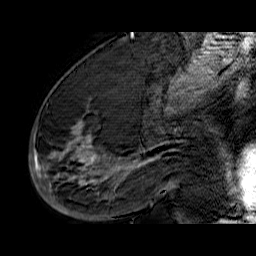
Breast MRI (dynamic contrast-enhanced), one sagittal slice; position 34 of 60 along the scan axis; dynamic contrast-enhanced series, time point 2 of 6 at this slice position (early post-contrast); 1.5 T; TE 6.5 ms, TR 32.9 ms; 4 mm slice thickness; 256 × 256 image matrix, field of view 200 × 200 mm. Female patient. Case-level facts recorded for this patient, not image findings: setting: breast cancer imaged before/during neoadjuvant chemotherapy; receptor status: HR-positive, HER2-negative.
Outlined on this slice (semi-automatically segmented with operator editing):
- analysis volume of interest (the breast-tissue region the enhancement analysis was run in; not a lesion): bounding box <33,74,176,210> (left, top, right, bottom; pixels)
- tumour enhancement mask (voxels above the 100 % enhancement threshold inside the analysis volume of interest): <33,130,172,190>